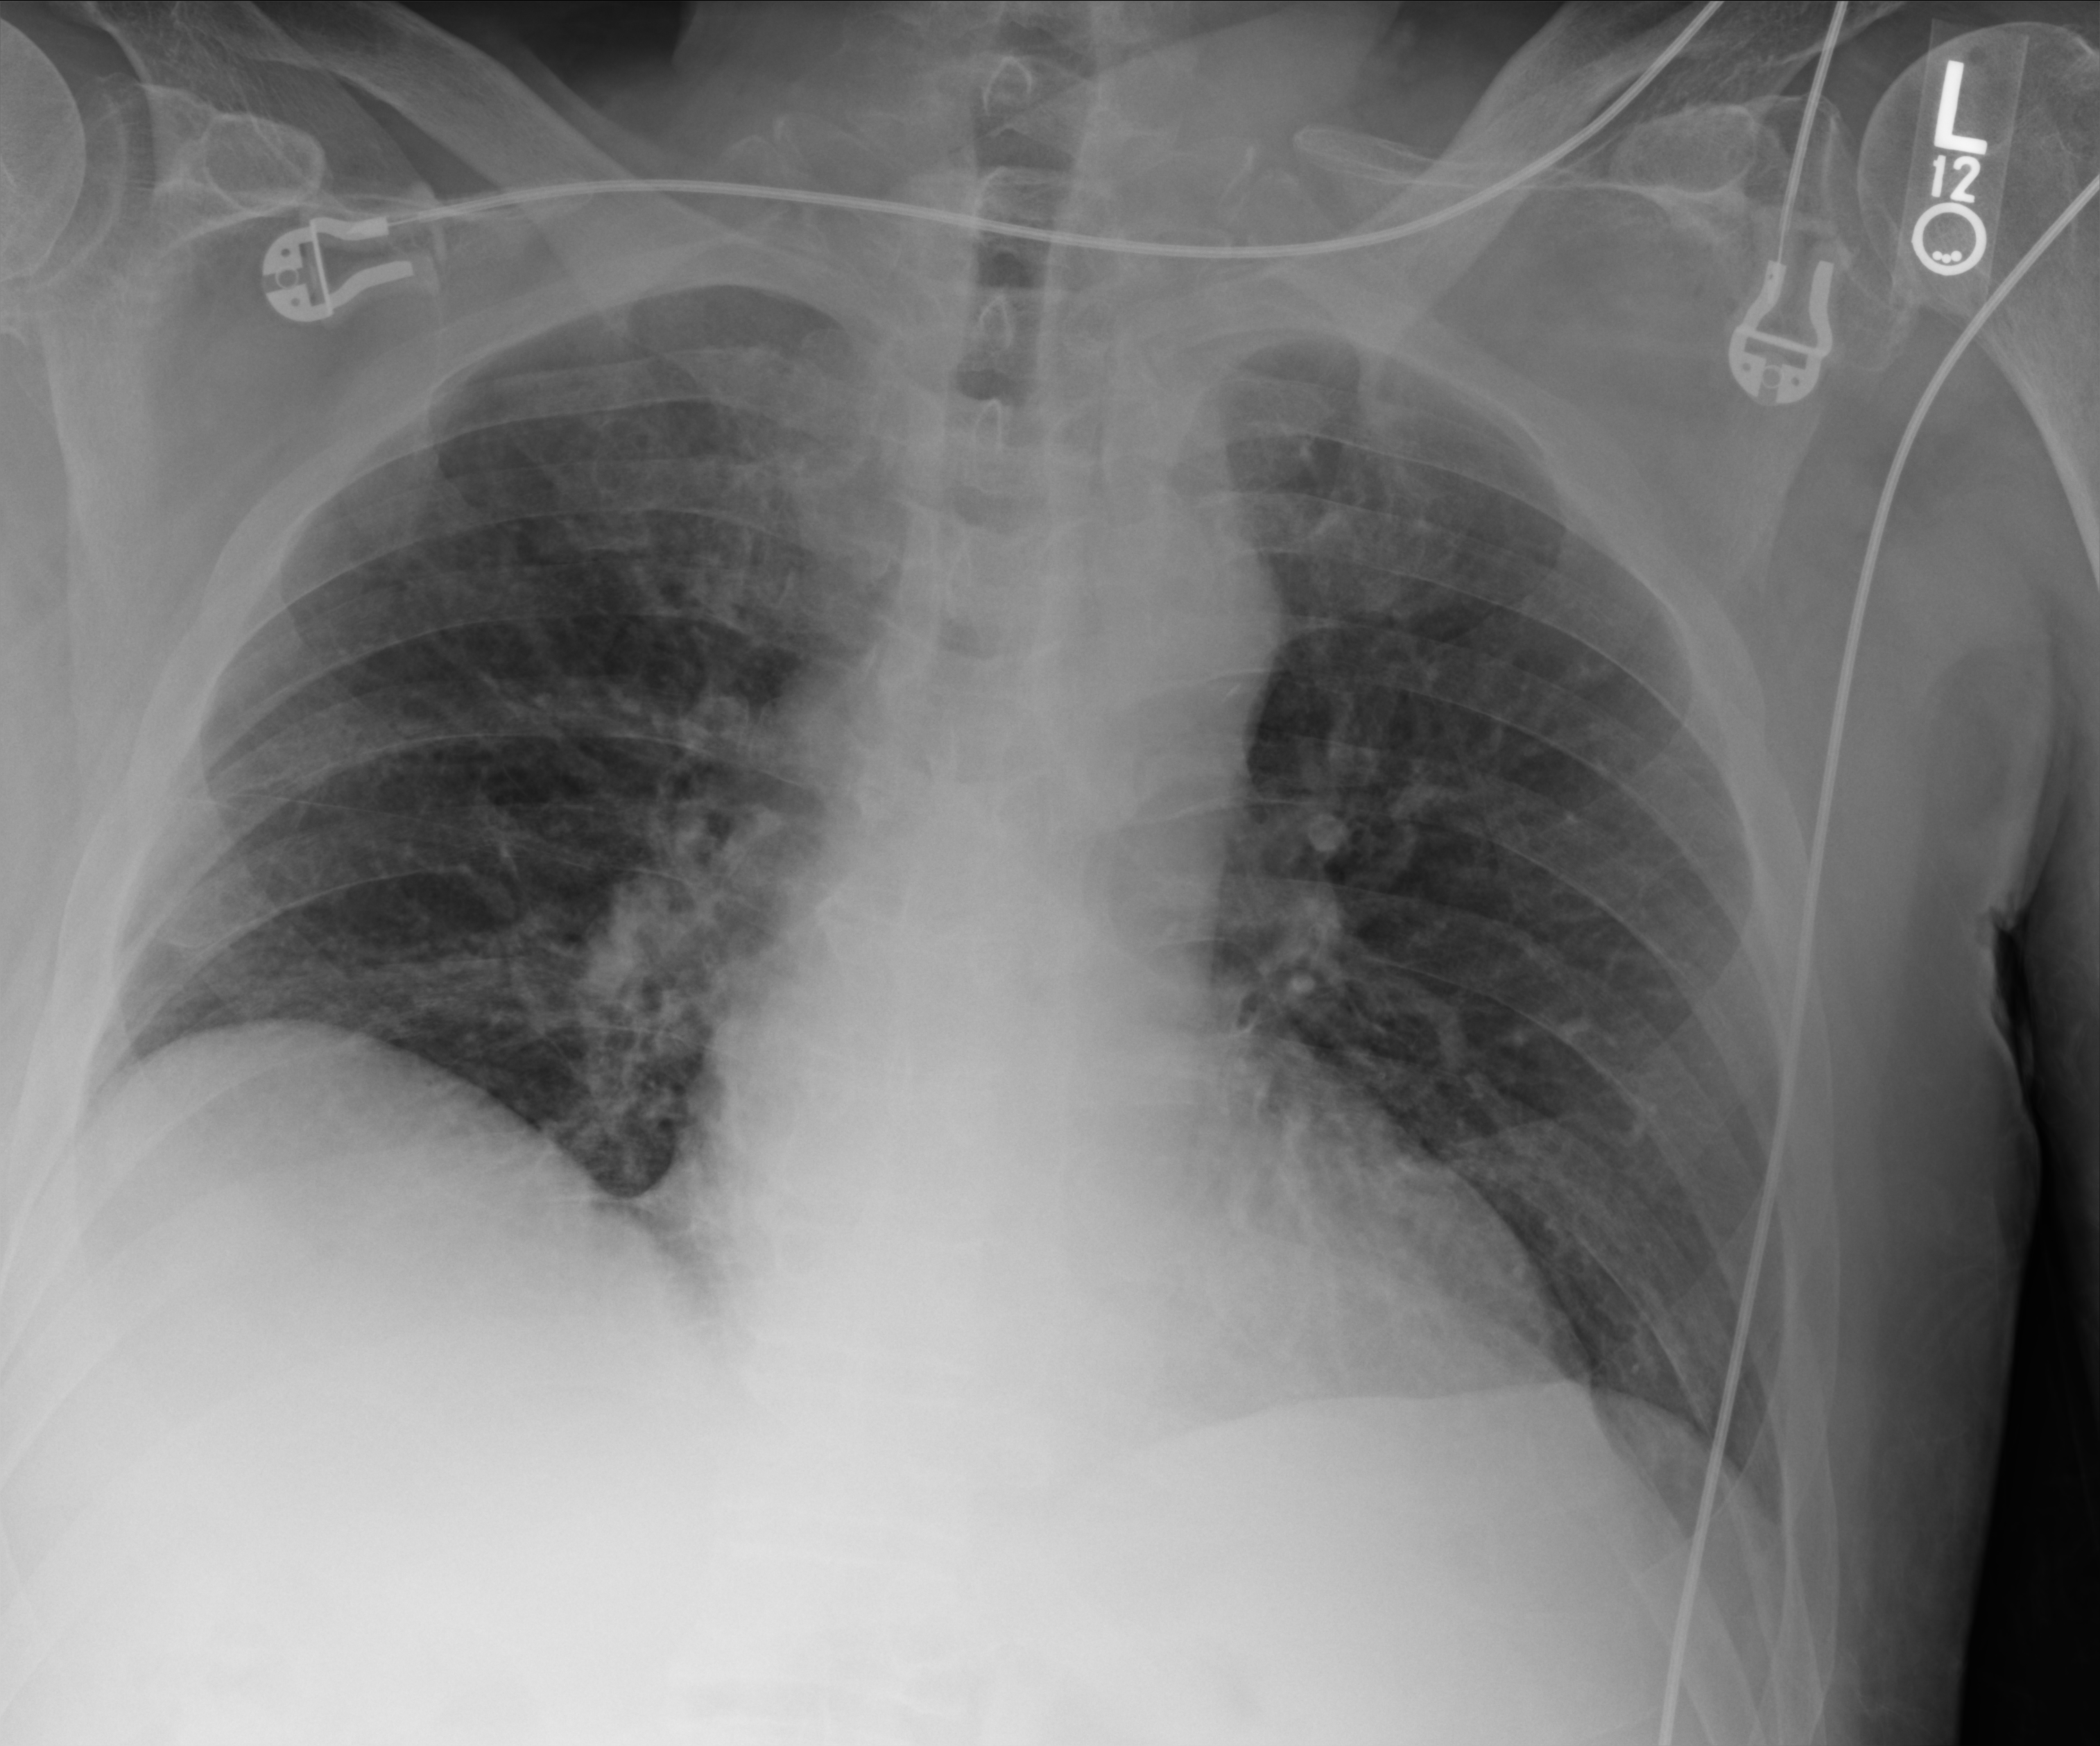
Chest X-ray (portable); anteroposterior (AP) projection. Patient hospitalised with COVID-19; male, aged 60–74 years.
Admission-level facts for this patient (not findings on this image; timing relative to this image not recorded):
- hypertension (admission record): yes
- smoking status (admission record): never
- admitted to intensive care during this hospital stay: no